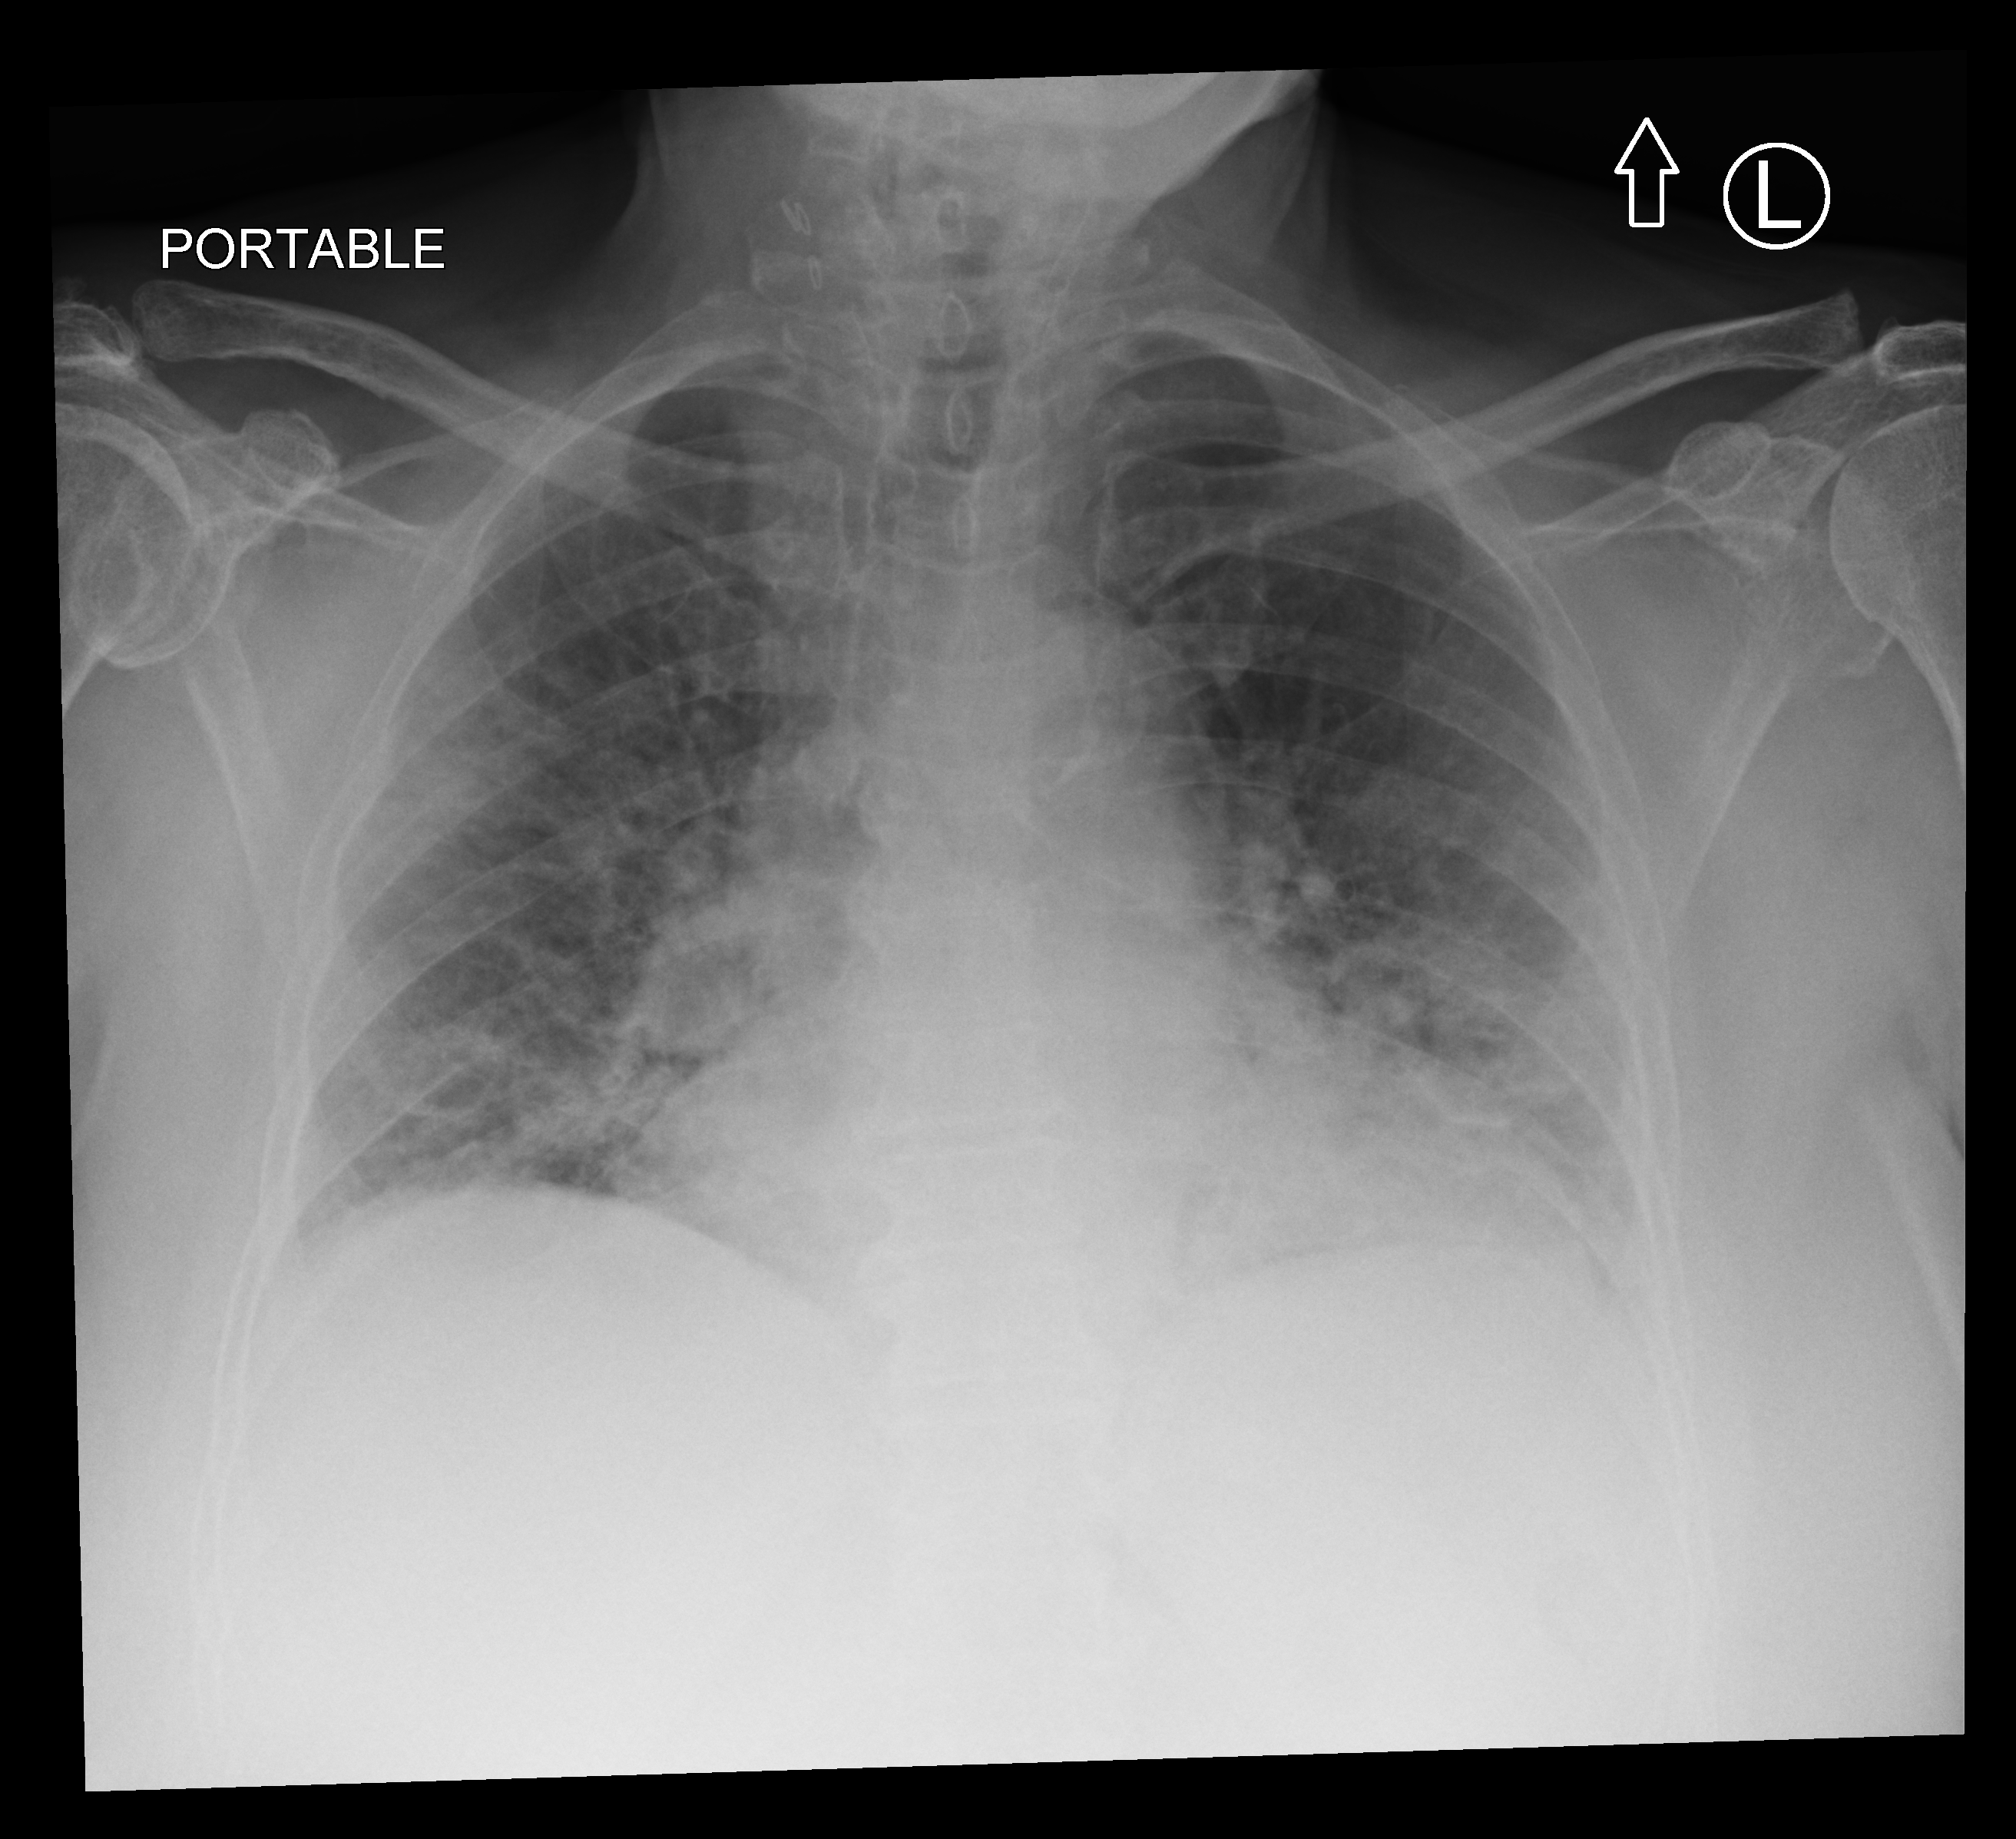
Chest X-ray (portable), anteroposterior (AP) projection. Patient hospitalised with COVID-19; female, aged 75–90 years.
Admission-level facts for this patient (not findings on this image; timing relative to this image not recorded):
- length of hospital stay: 8 days
- diabetes (admission record): yes
- admitted to intensive care during this hospital stay: no